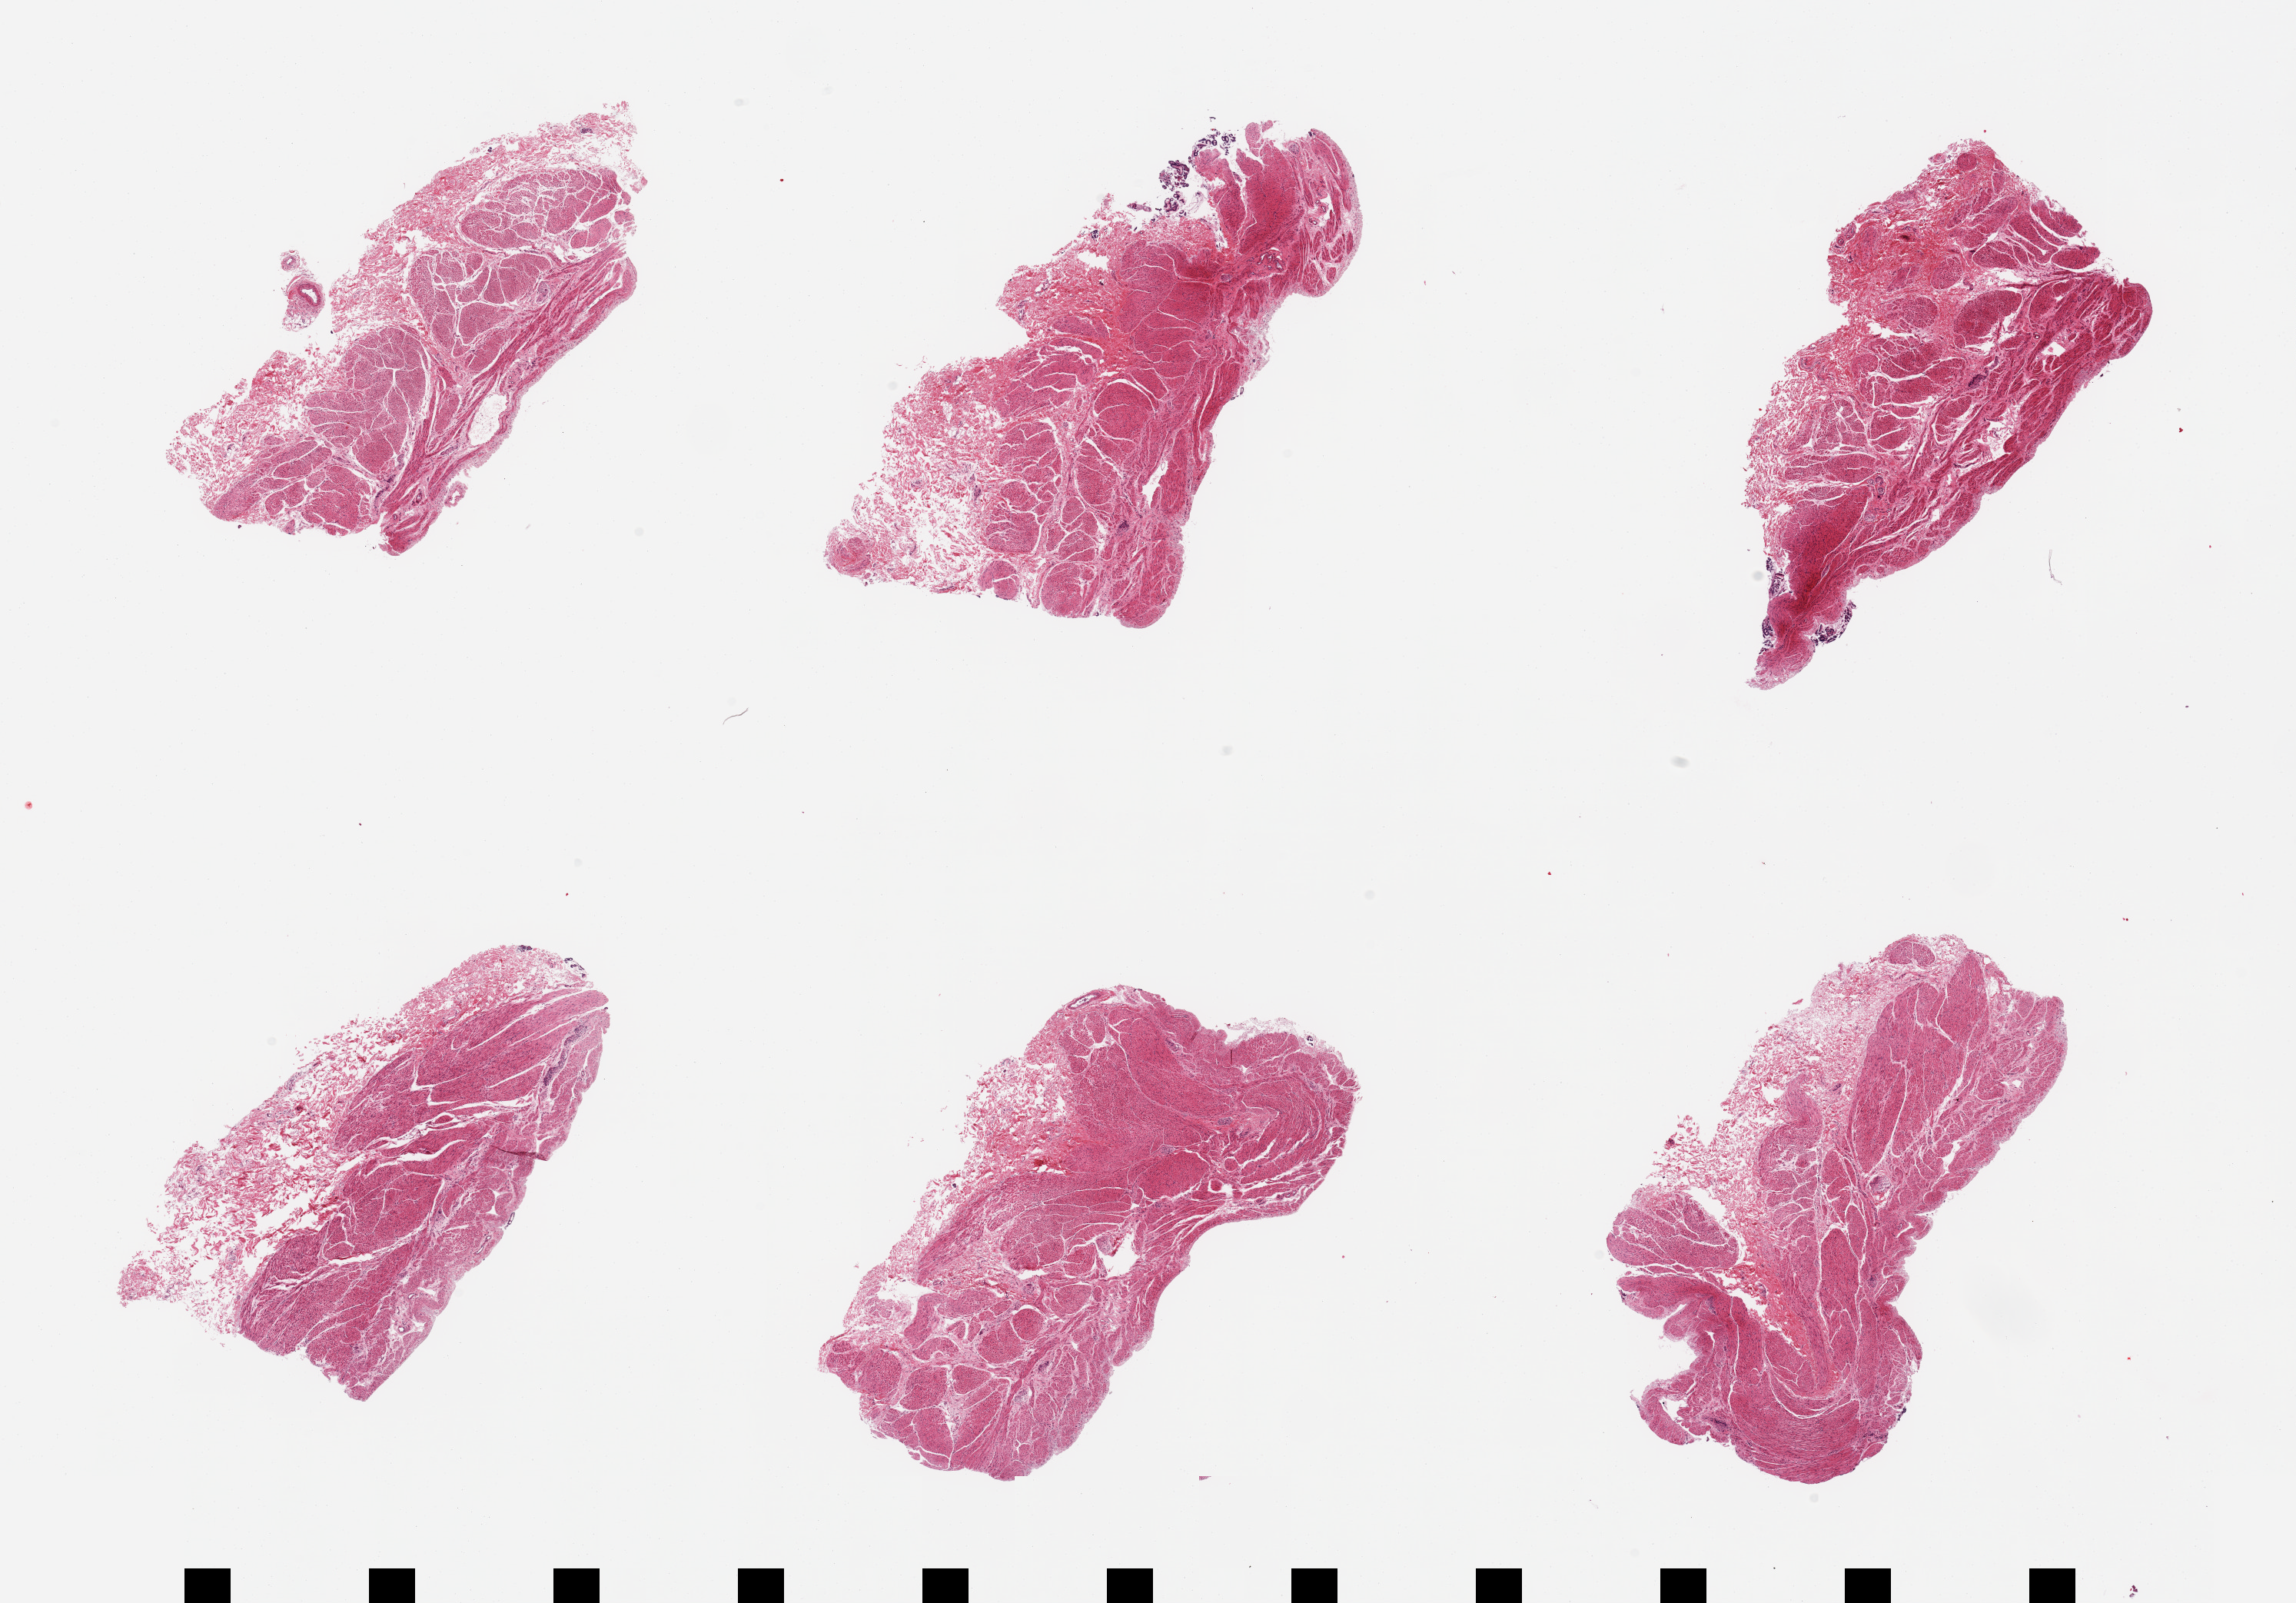
Whole-slide image, hematoxylin and eosin (H&E) stain — low-resolution overview of the scanned area, about 23.6 x 16.5 mm, PAXgene-fixed, paraffin-embedded tissue, target tissue: stomach, donor tissue sample. Donor: male.
* pathologist's review note for this sample: 6 pieces; MUSCULARIS, NOT STOMACH, up to ~1.3mm attached fibrofatty tissue